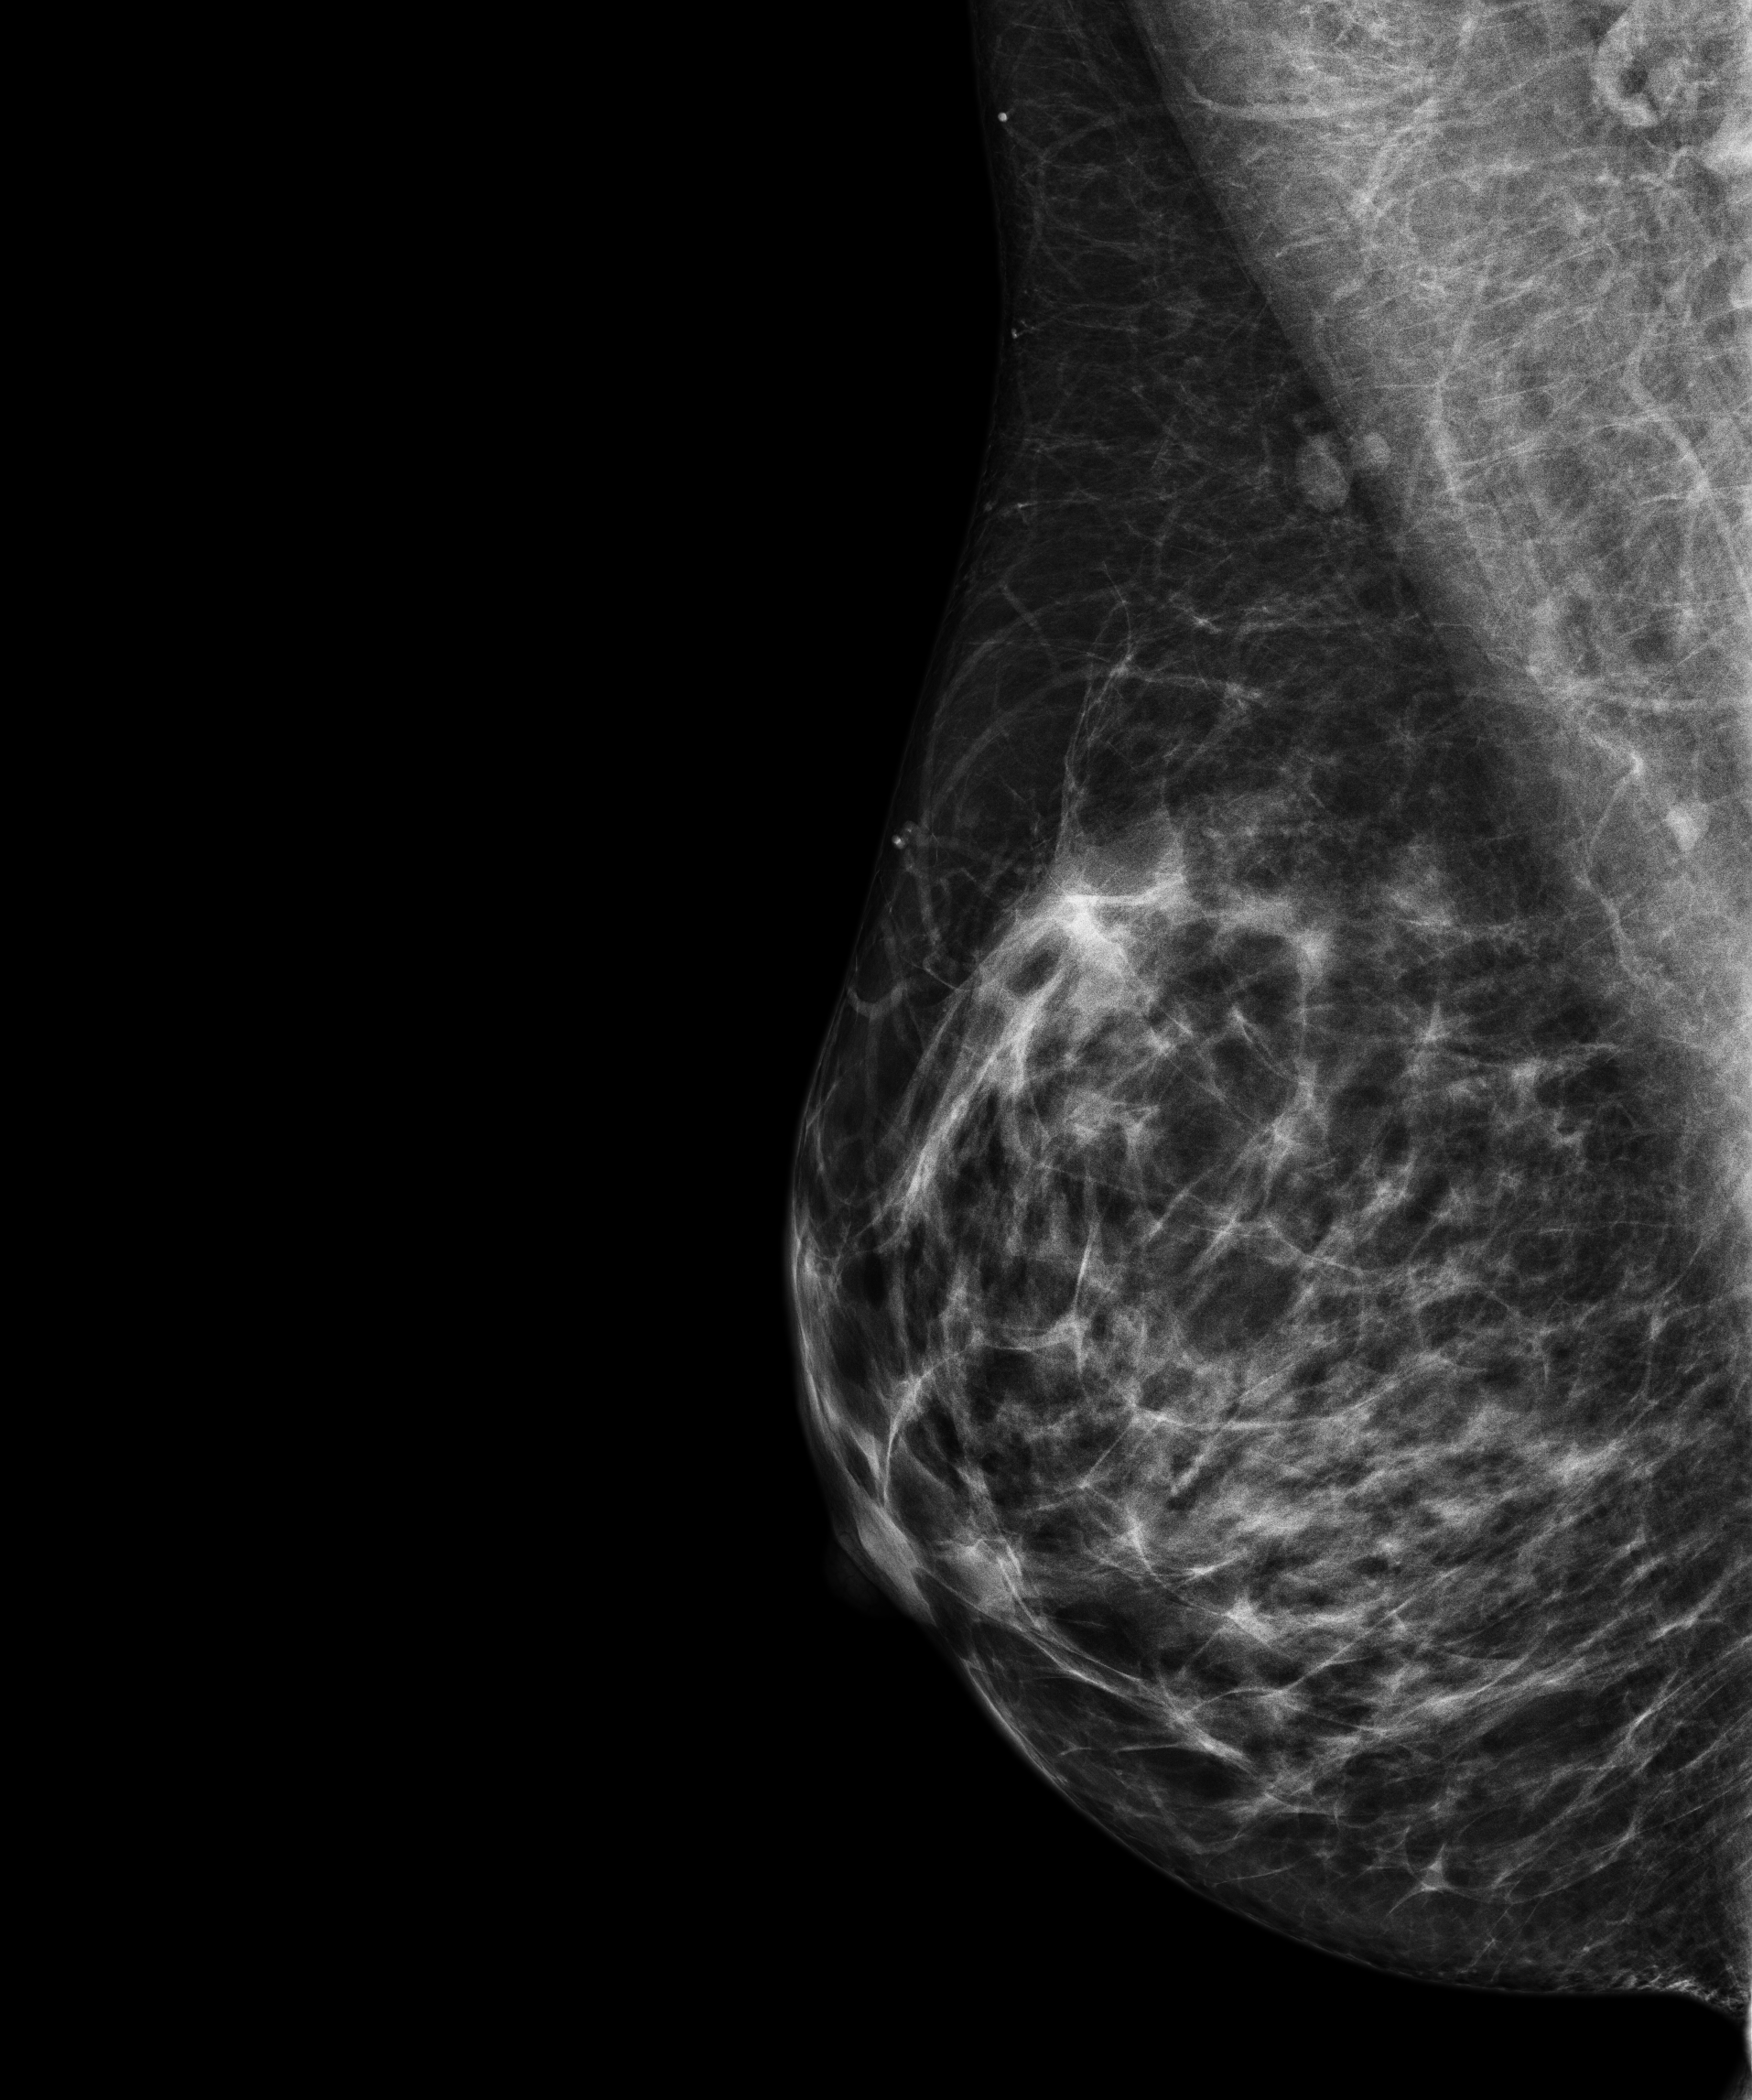
Annual screening mammography examination, compressed breast thickness 67.4 mm, system: Senographe Pristina. Female patient, age 46 years.
Image type: full-field digital mammogram. Breast: right. Projection: MLO view.